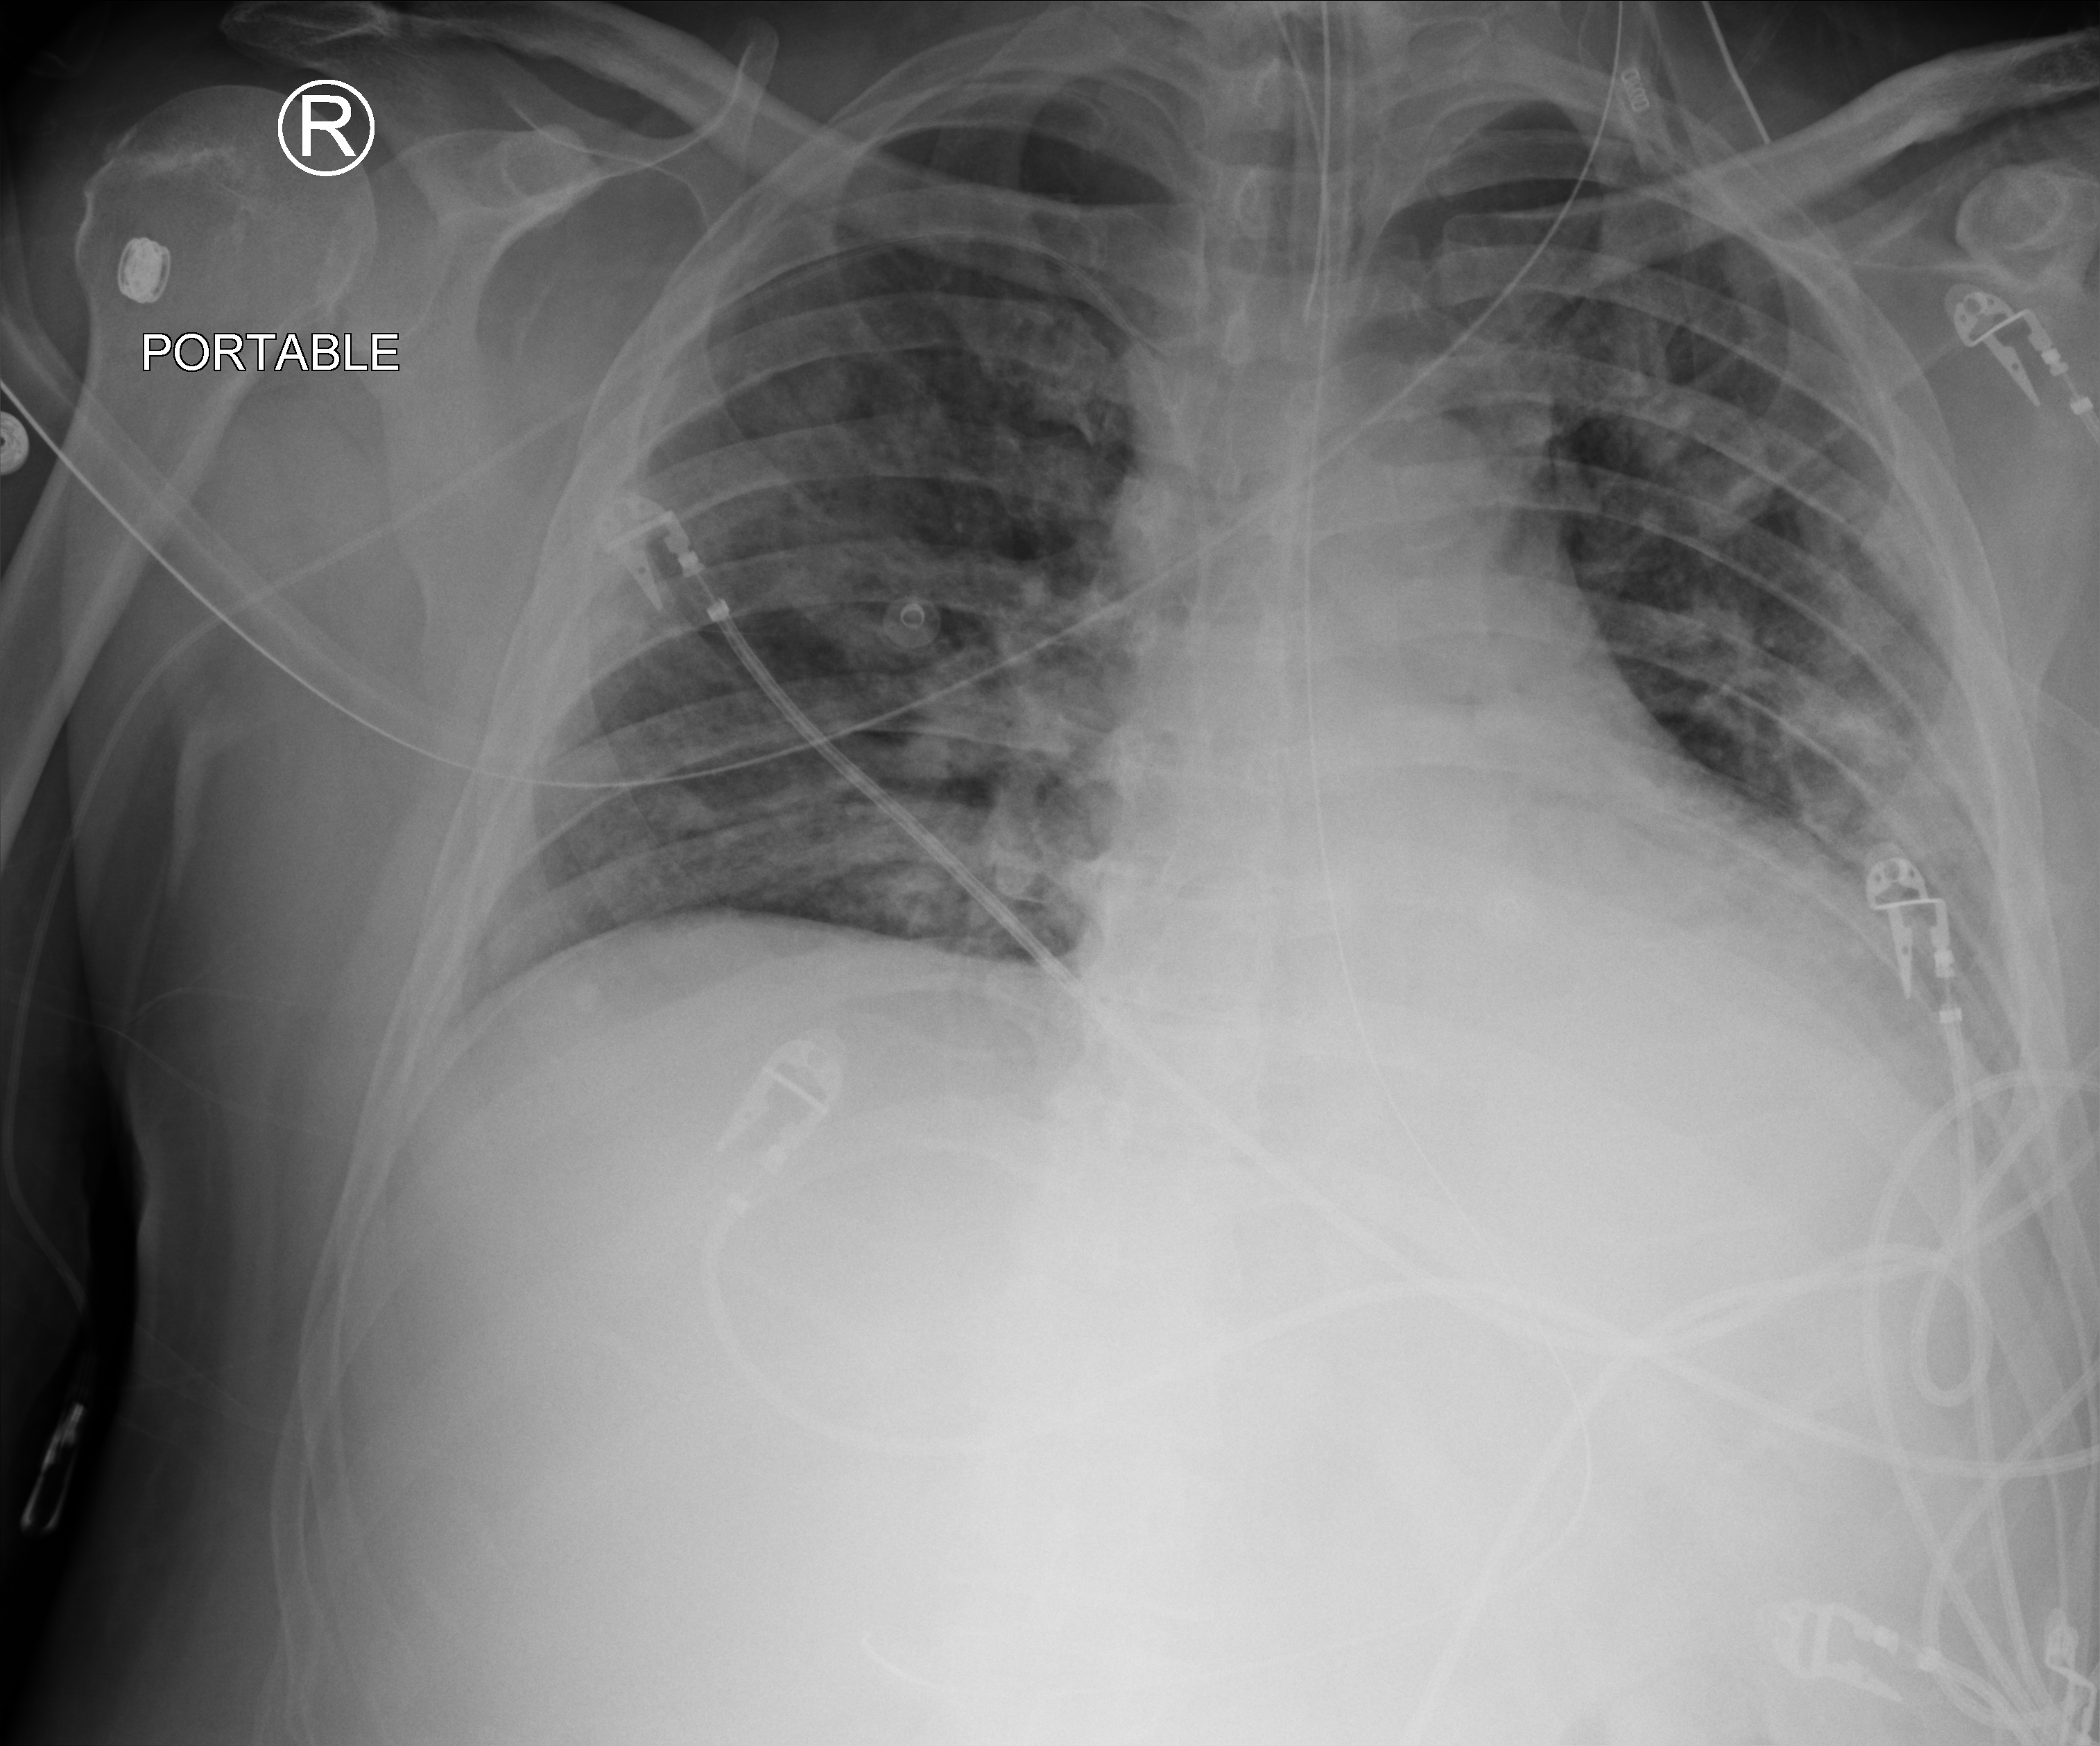
Portable chest radiograph, anteroposterior (AP) projection. Patient hospitalised with COVID-19; male, aged 18–59 years.
Admission-level facts for this patient (not findings on this image; timing relative to this image not recorded): other chronic lung disease (admission record): no; length of hospital stay: 30 days.